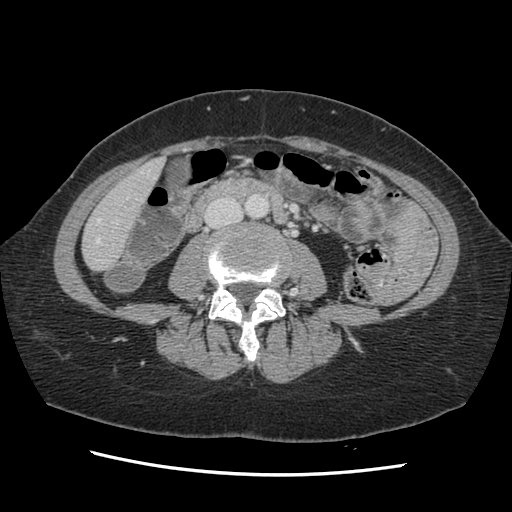
Contrast-enhanced abdominal CT, one axial slice. Slice 31 of 141 in the series (ordered by position). 120 kVp. Soft-tissue window (W 400 / L 40 HU). 2.5 mm slice thickness. 512 × 512 image matrix, field of view 330 × 330 mm. Female patient, age 61 years. From the clinical record (not read from this slice): diagnosis: colorectal cancer liver metastases, imaged before liver resection; multiple liver metastases: no; largest metastasis: 2.4 cm.
Structures marked on this image (manually delineated by an expert):
- hepatic veins: bounding box (x1, y1, x2, y2) in pixels: (96, 170, 155, 243)
- liver: (84, 160, 162, 271)
- planned liver remnant (the part of the liver to remain after resection): (84, 161, 162, 271)